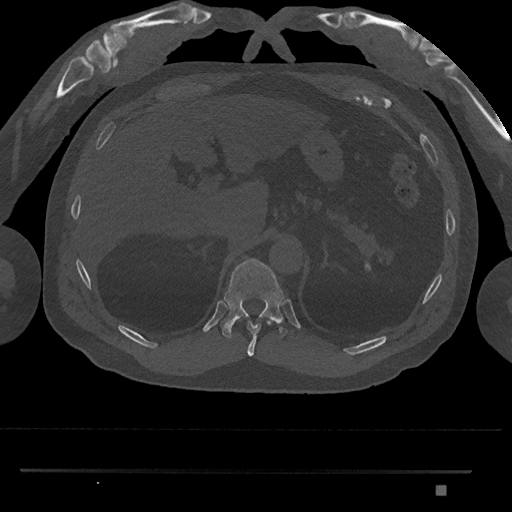
CT including the spine, one axial slice; slice 966 of 1134 in the series (ordered by position); reconstruction kernel Br40s/3; bone window (W 1800 / L 400 HU); 0.5 mm slice thickness; 512 × 512 image matrix. Patient: male, 65 years. Case-level facts recorded for this patient, not image findings: primary cancer: prostate.
Annotated regions visible in this slice (semi-automatic segmentation, software-assisted and operator-edited):
- T10 vertebra: bounding box (x1, y1, x2, y2) in pixels: (247, 321, 261, 356)
- T11 vertebra: (220, 258, 288, 339)